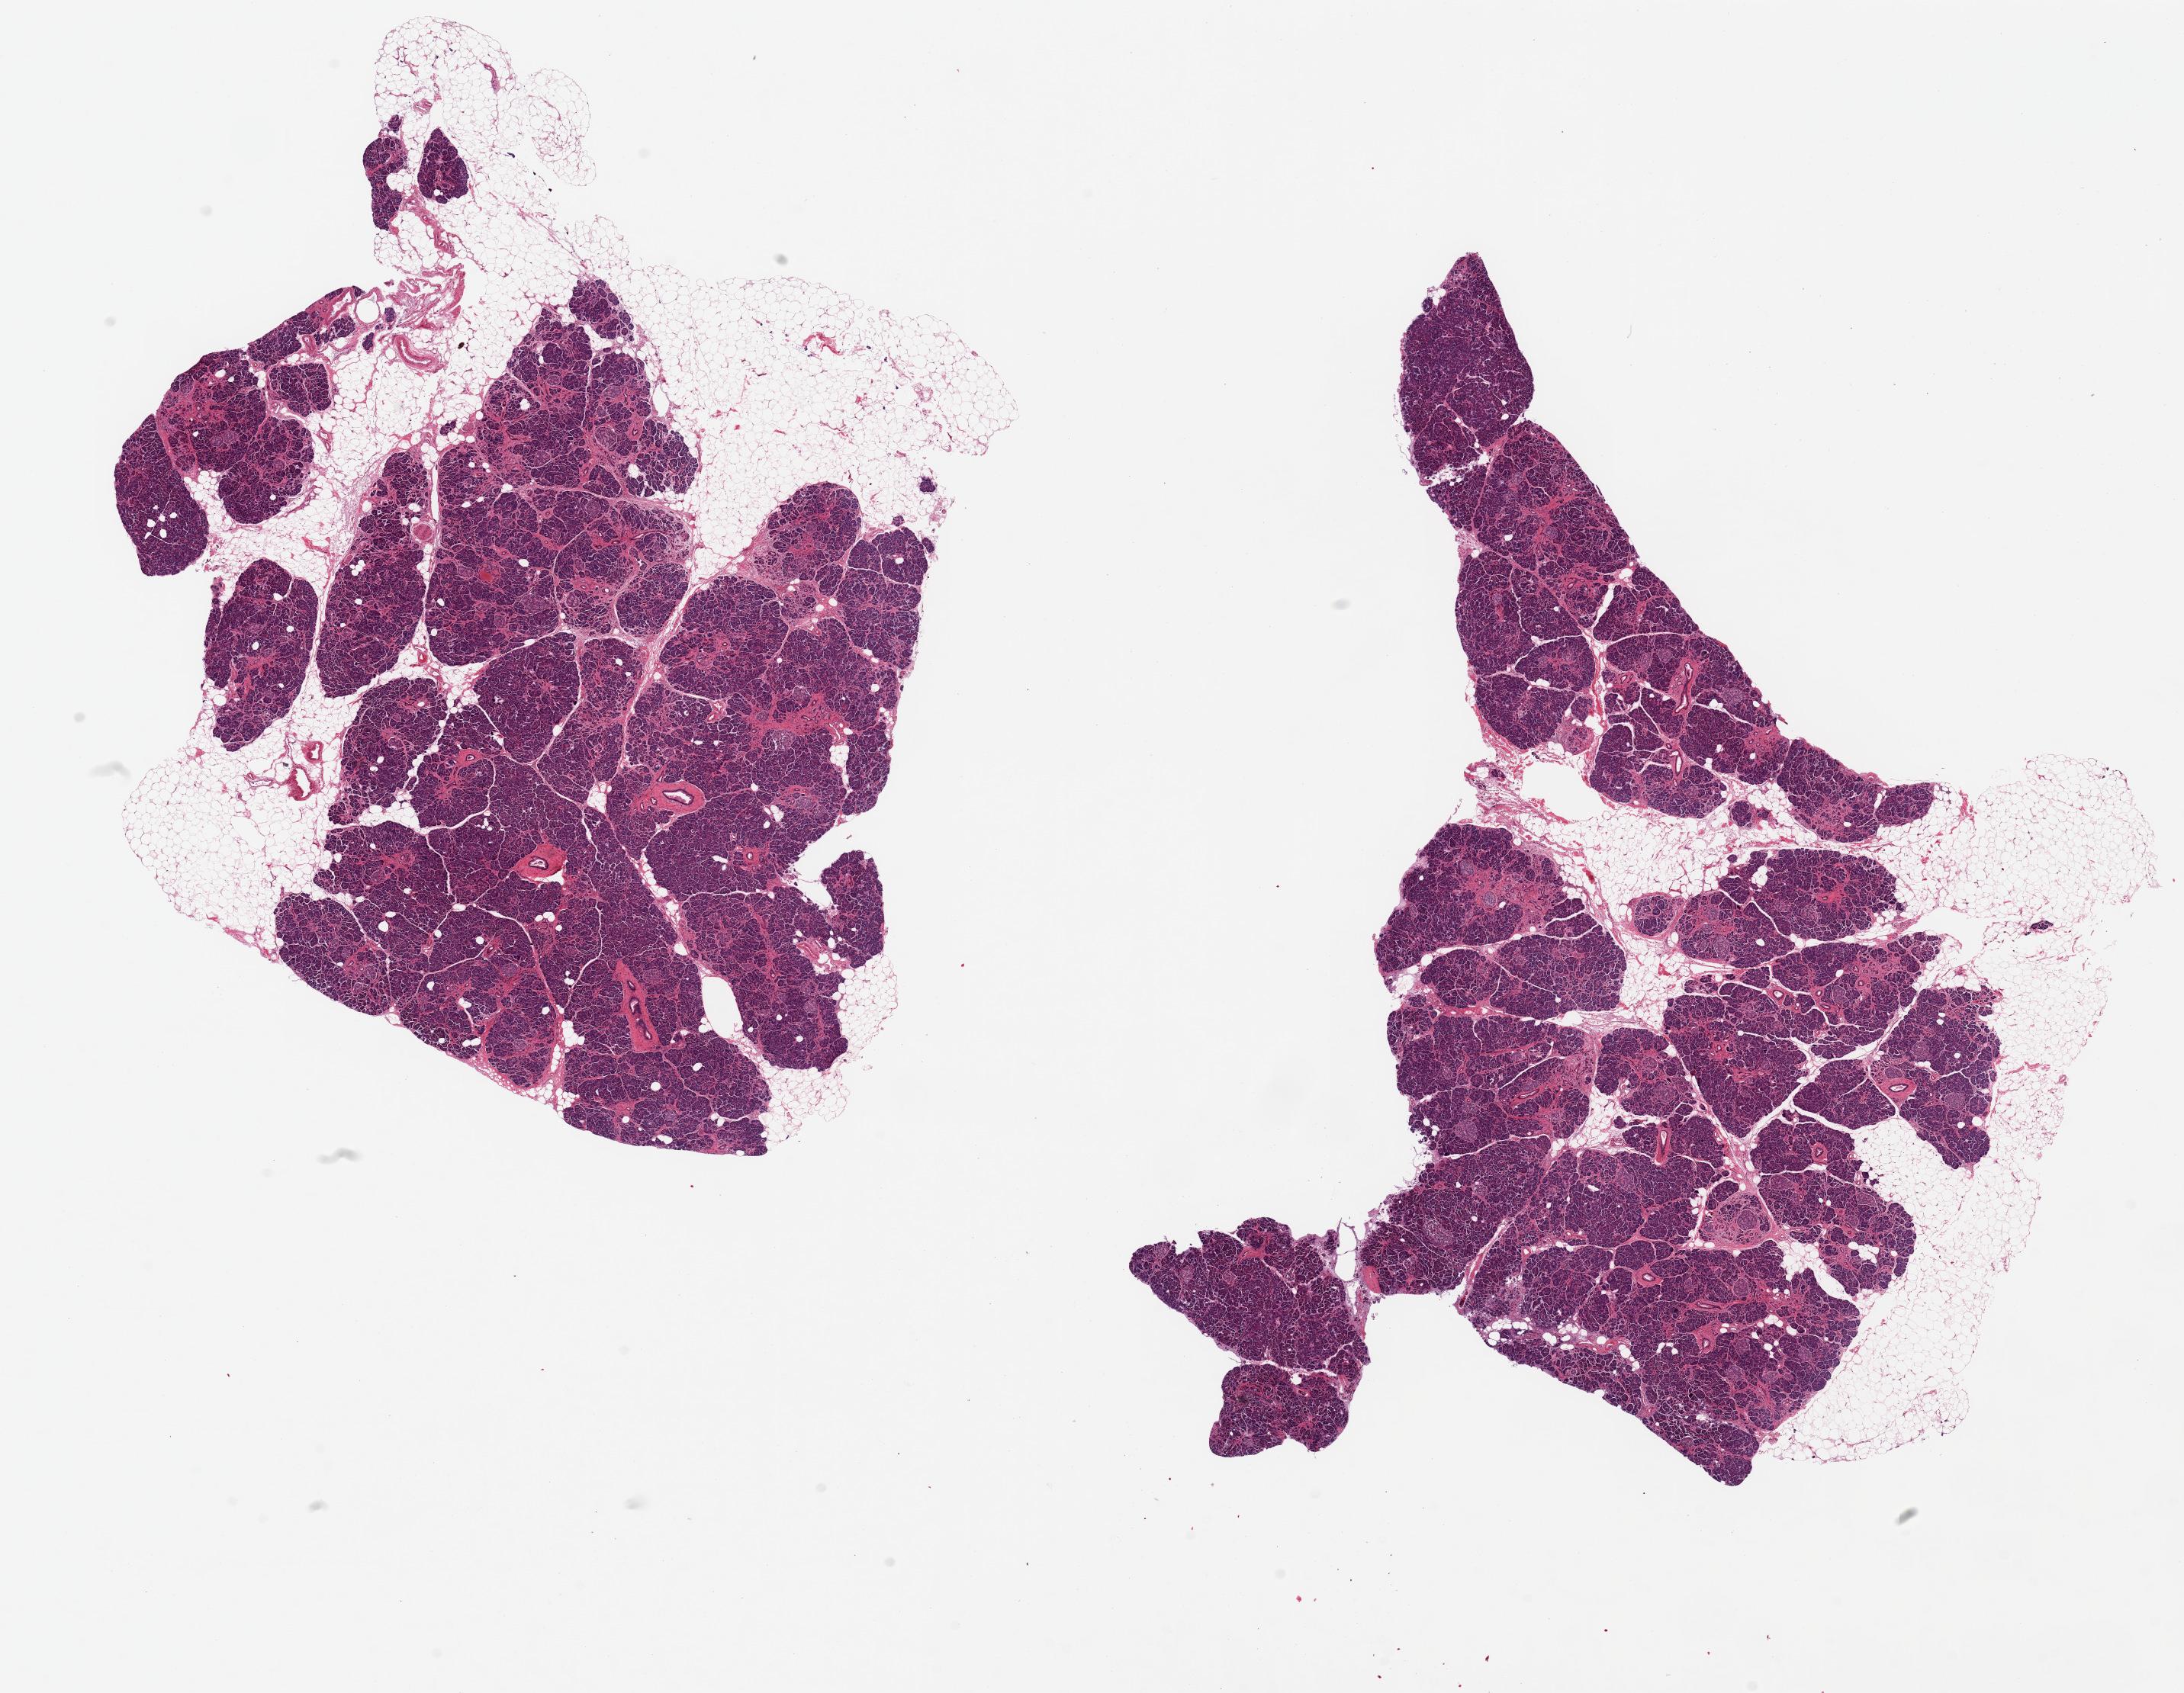
Whole-slide image, haematoxylin and eosin stain, brightfield — low-resolution overview of the scanned area, about 22.6 x 17.6 mm, PAXgene-fixed paraffin-embedded (PFPE) section, sampled site (target tissue): pancreas, tissue donor sample. Donor: male.
Review note (as recorded): 2 pieces ~9x7mm. ~80% well-preserved parenchyma, deliniated ,rest adherent fat up to ~1.5mm thick.